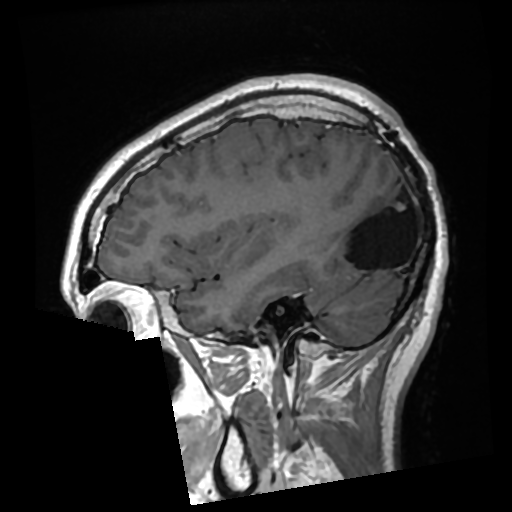
Brain MRI from a brain-tumour surgery series, one sagittal slice. Position 88 of 276 along the scan axis. T1-weighted post-contrast. 0.7 mm slice thickness. 512 × 512 image matrix, field of view 250 × 250 mm. From the clinical record (not read from this slice): histopathology: Glioma with ependymal features; WHO grade: 2; tumour location: Left Parietal.
Annotated regions visible in this slice (expert manual segmentation):
- previous resection cavity: bounding box [x1, y1, x2, y2] px = [336, 182, 410, 270]
- tumour: [397, 204, 405, 210]